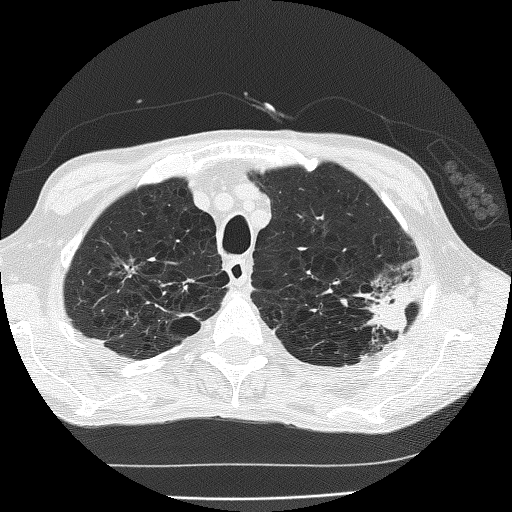
Low-dose screening chest CT, one axial slice. Position 152 of 185 along the scan axis. Reconstruction kernel FC51. Lung window (W 1500 / L -600 HU). 2 mm slice thickness. 512 × 512 image matrix.
Structures marked on this image (expert manual segmentation):
- lesion 1 (tumor, upper lobe of left lung): bounding box [x1, y1, x2, y2] px = [369, 280, 418, 333]